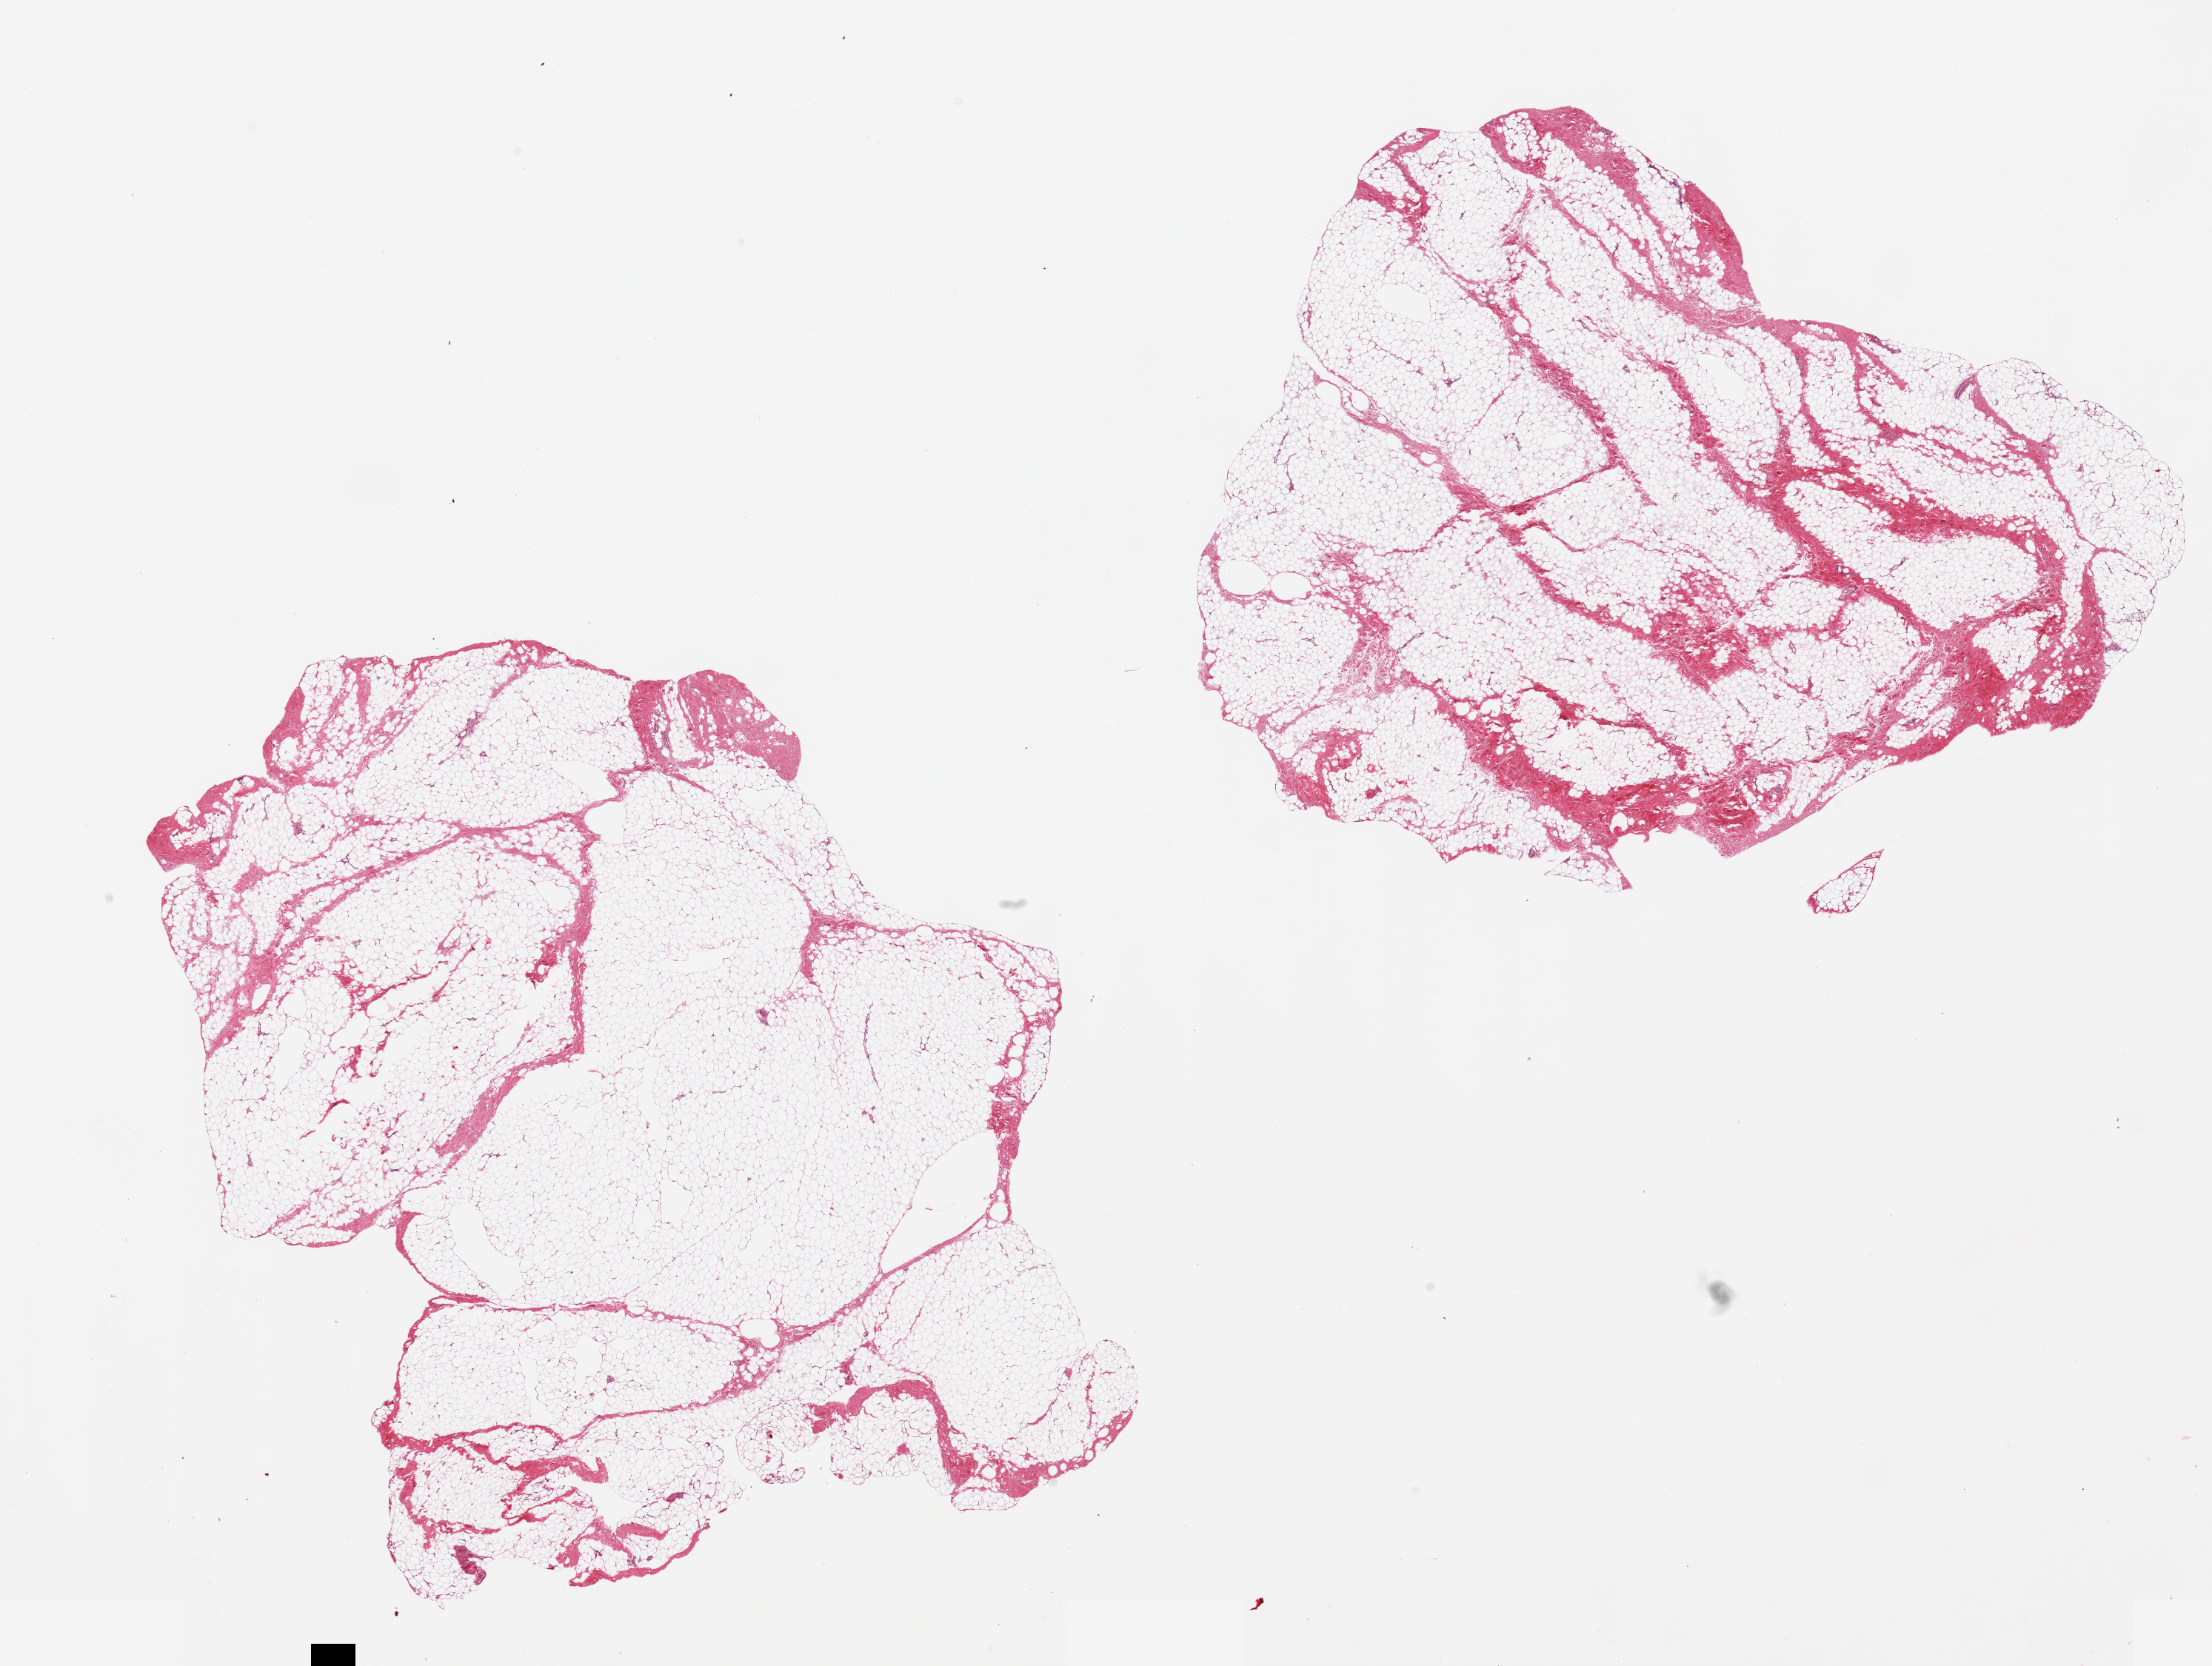
Digitized hematoxylin and eosin (H&E)-stained section — shown as a low-resolution overview of the whole scanned area (about 23.6 x 17.8 mm), PAXgene-fixed paraffin-embedded (PFPE) section, sampled site (target tissue): breast, tissue donor sample. Donor sex: male.
Pathologist's review note for this sample: 2 pieces, fibroadipose elements only.